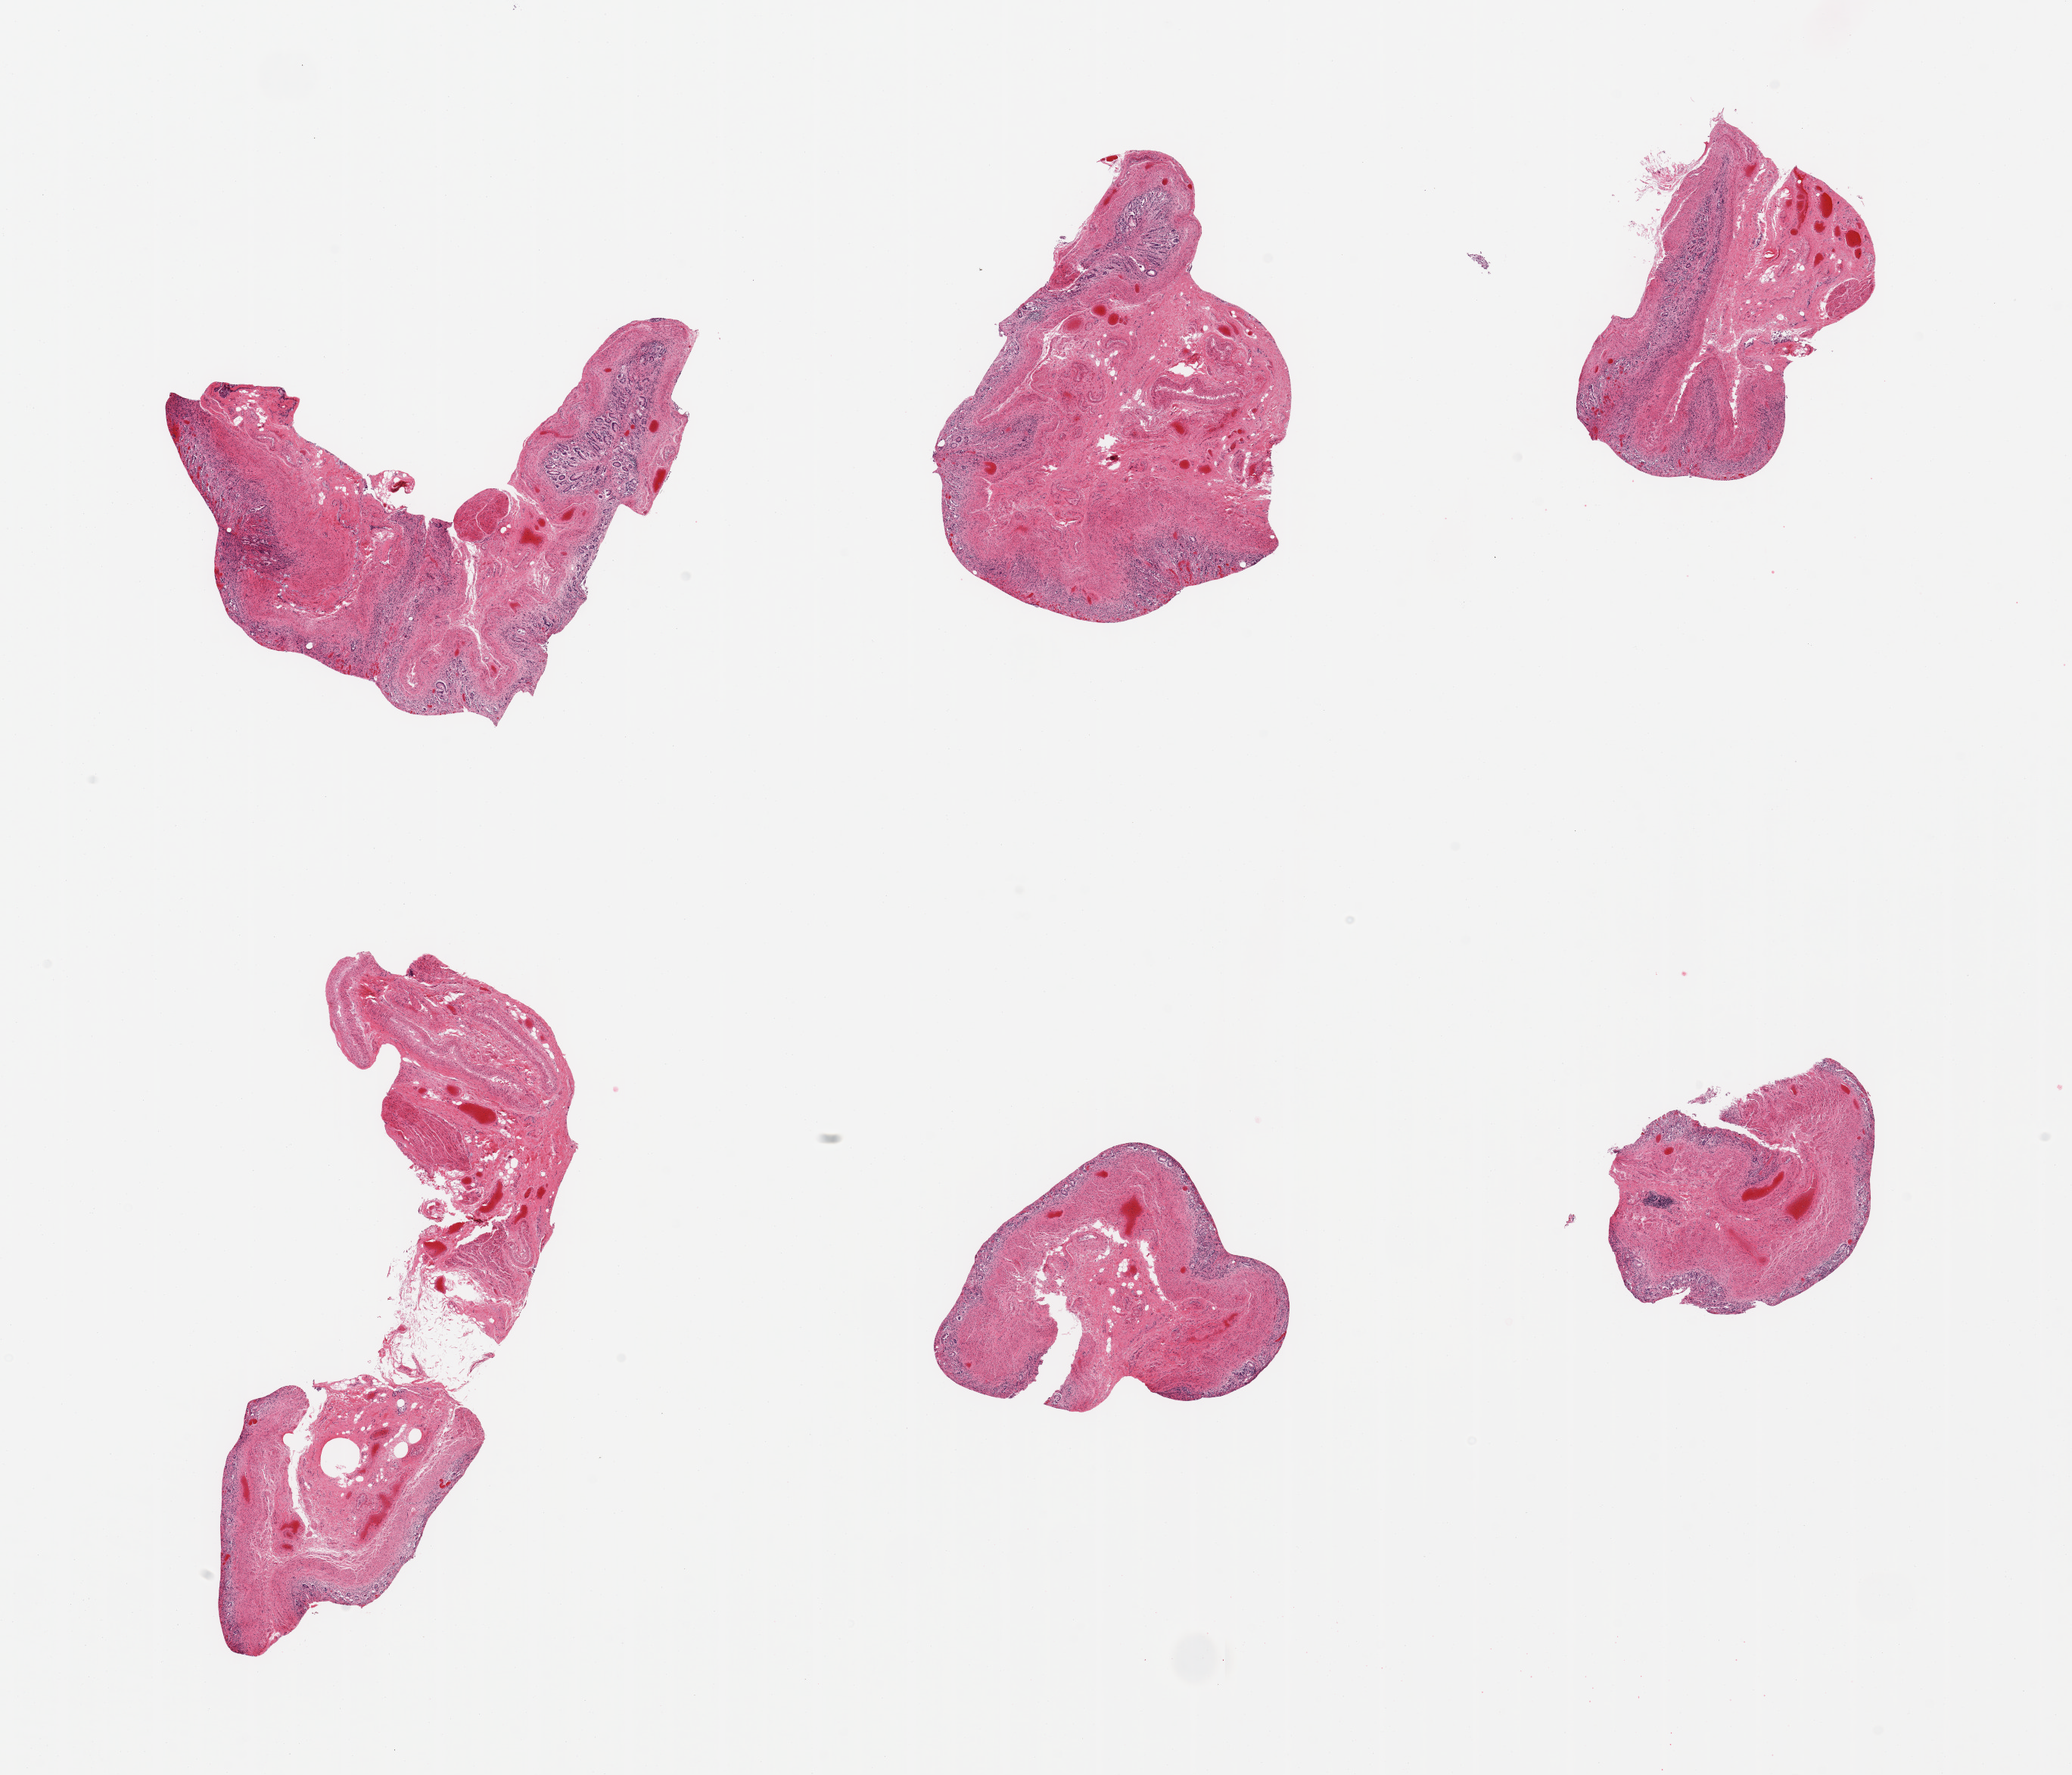
Hematoxylin and eosin (H&E) whole-slide image — whole scanned area (about 21.7 x 18.5 mm, acquisition: 20x scan) shown as a low-resolution overview; PAXgene-fixed, paraffin-embedded tissue; sampled site (target tissue): gastroesophageal junction; donor tissue sample. Male donor.
Review note (as recorded): 6 pieces; all contain autolyzed glandular mucosa, not muscularis.